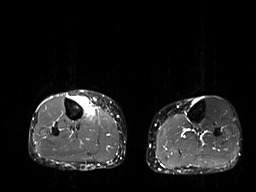
MRI of an extremity soft-tissue mass, one axial slice. Position 14 of 32 along the scan axis. STIR. 256 × 192 image matrix. Female patient. From the clinical record (not read from this slice): histological type: undifferentiated – high grade; grade: high; site of the primary tumour: right thigh.
Structures marked on this image (outlined manually by an expert reader):
- gross tumour volume (mass): bounding box <70,94,93,116> (left, top, right, bottom; pixels)